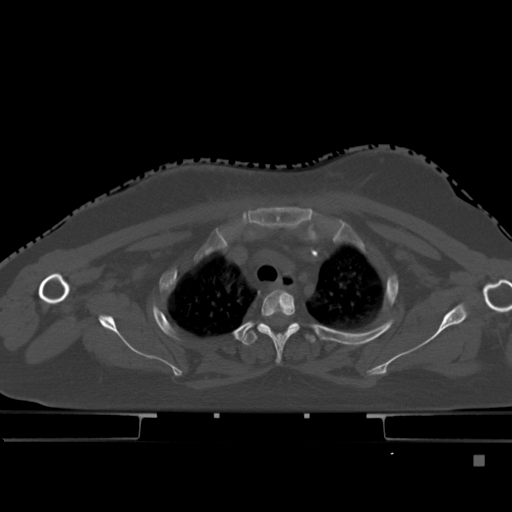
CT including the spine, one axial slice. Position 354 of 495 along the scan axis. Bone window (W 1800 / L 400 HU). 1.5 mm slice thickness. 512 × 512 image matrix, field of view 404 × 404 mm. Patient: female, 33 years. Case-level facts recorded for this patient, not image findings: primary cancer: breast; vertebrae with lytic lesions (as recorded): T1.
Structures marked on this image (semi-automatic segmentation, software-assisted and operator-edited):
- T2 vertebra: bounding box (x1, y1, x2, y2) in pixels: (258, 290, 300, 362)
- T3 vertebra: (242, 322, 316, 346)